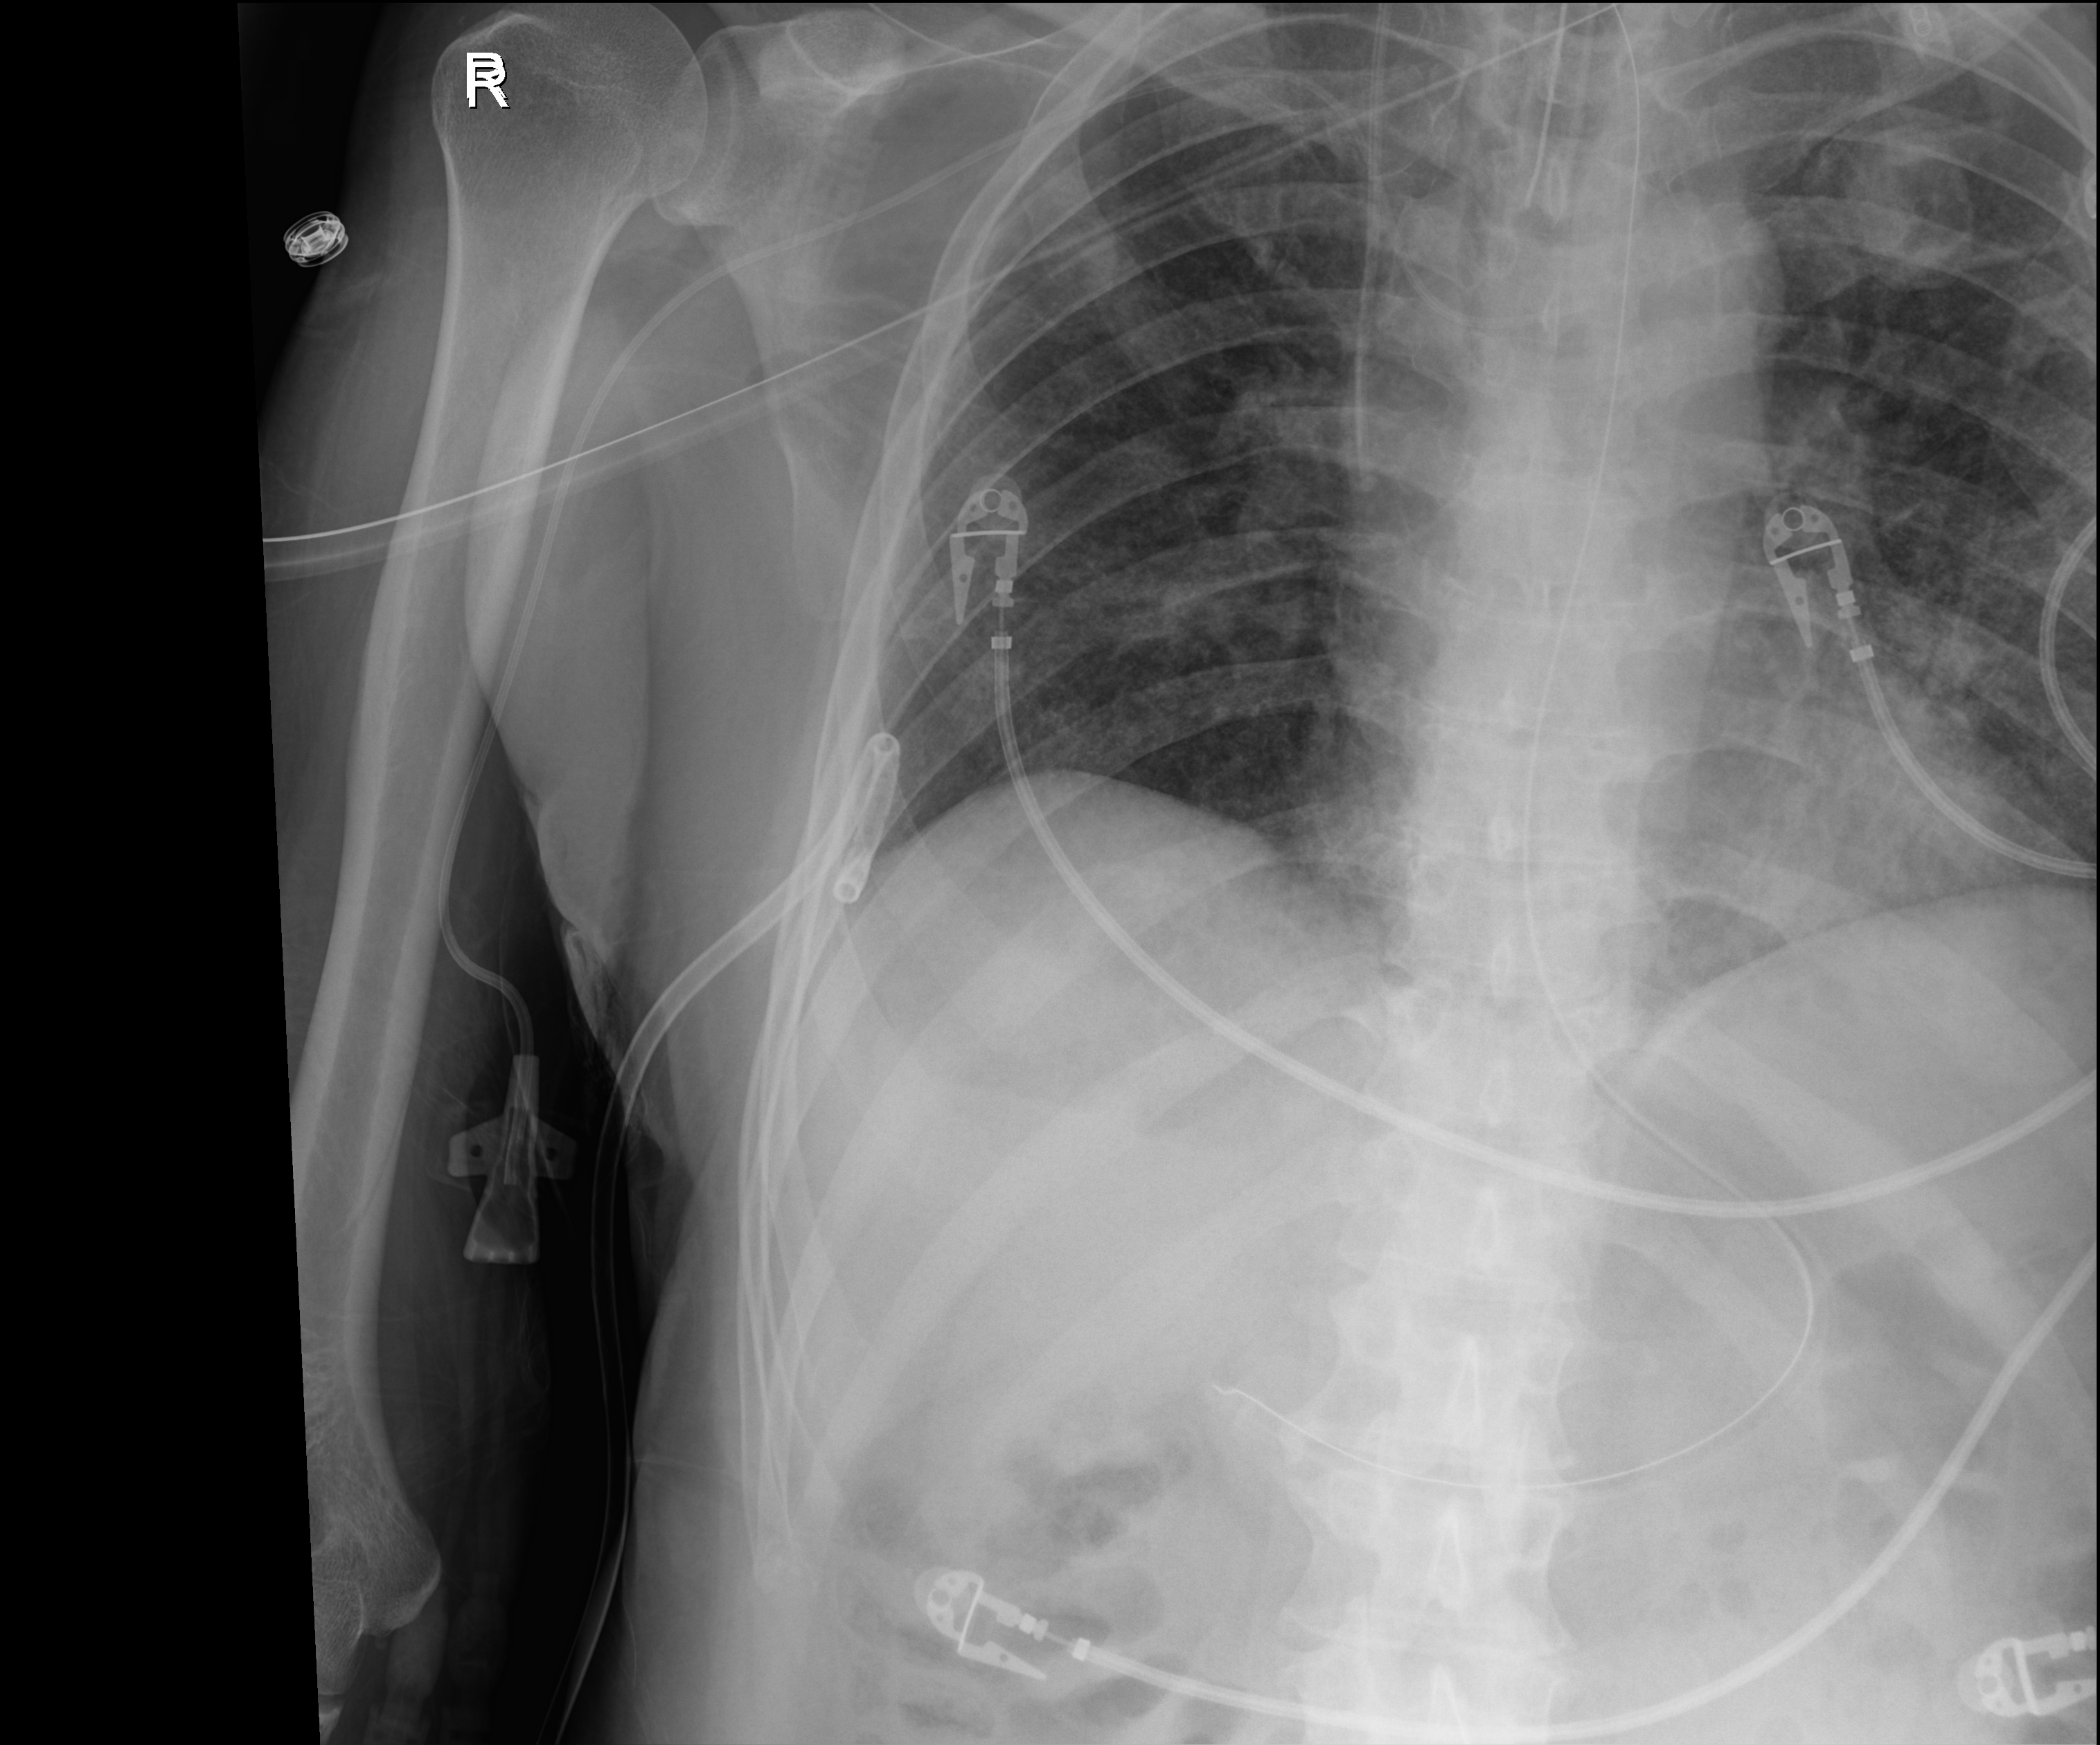
Portable chest radiograph; anteroposterior (AP) projection. Male patient hospitalised with COVID-19, age 18–59 years.
Hospital-stay facts (about this admission, not read from this image; timing relative to this image not recorded):
- admitted to intensive care during this hospital stay: yes
- diabetes (admission record): no